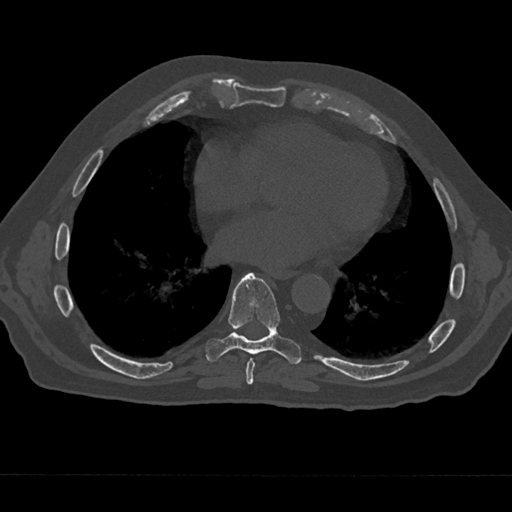
CT including the spine, one axial slice; slice 322 of 797 in the series (ordered by position); reconstruction kernel Br40s/3; 120 kVp; bone window (W 1800 / L 400 HU); 512 × 512 image matrix. Male patient, age 75 years. Case-level facts recorded for this patient, not image findings: primary cancer: renal.
Annotated regions visible in this slice (semi-automatic segmentation, software-assisted and operator-edited):
- T7 vertebra: bounding box [x1, y1, x2, y2] px = [244, 357, 258, 385]
- T8 vertebra: [205, 273, 301, 365]